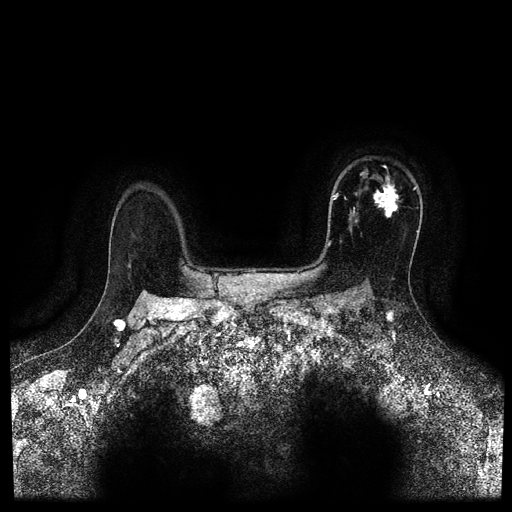
Breast MRI (dynamic contrast-enhanced, multi-phase), one axial slice. Dynamic contrast-enhanced series, time point 2 of 5 at this slice position (early post-contrast). 1.5 T. TE 2.7 ms, TR 5.4 ms. 2 mm slice thickness. 512 × 512 image matrix. Female patient, age 50 years.
Annotated regions visible in this slice (semi-automatic segmentation, software-assisted and operator-edited):
- breast lesion (labelled 'tumour' in the annotation; benign lesions carry a separate 'benign' label): bounding box <372,177,404,219> (left, top, right, bottom; pixels)